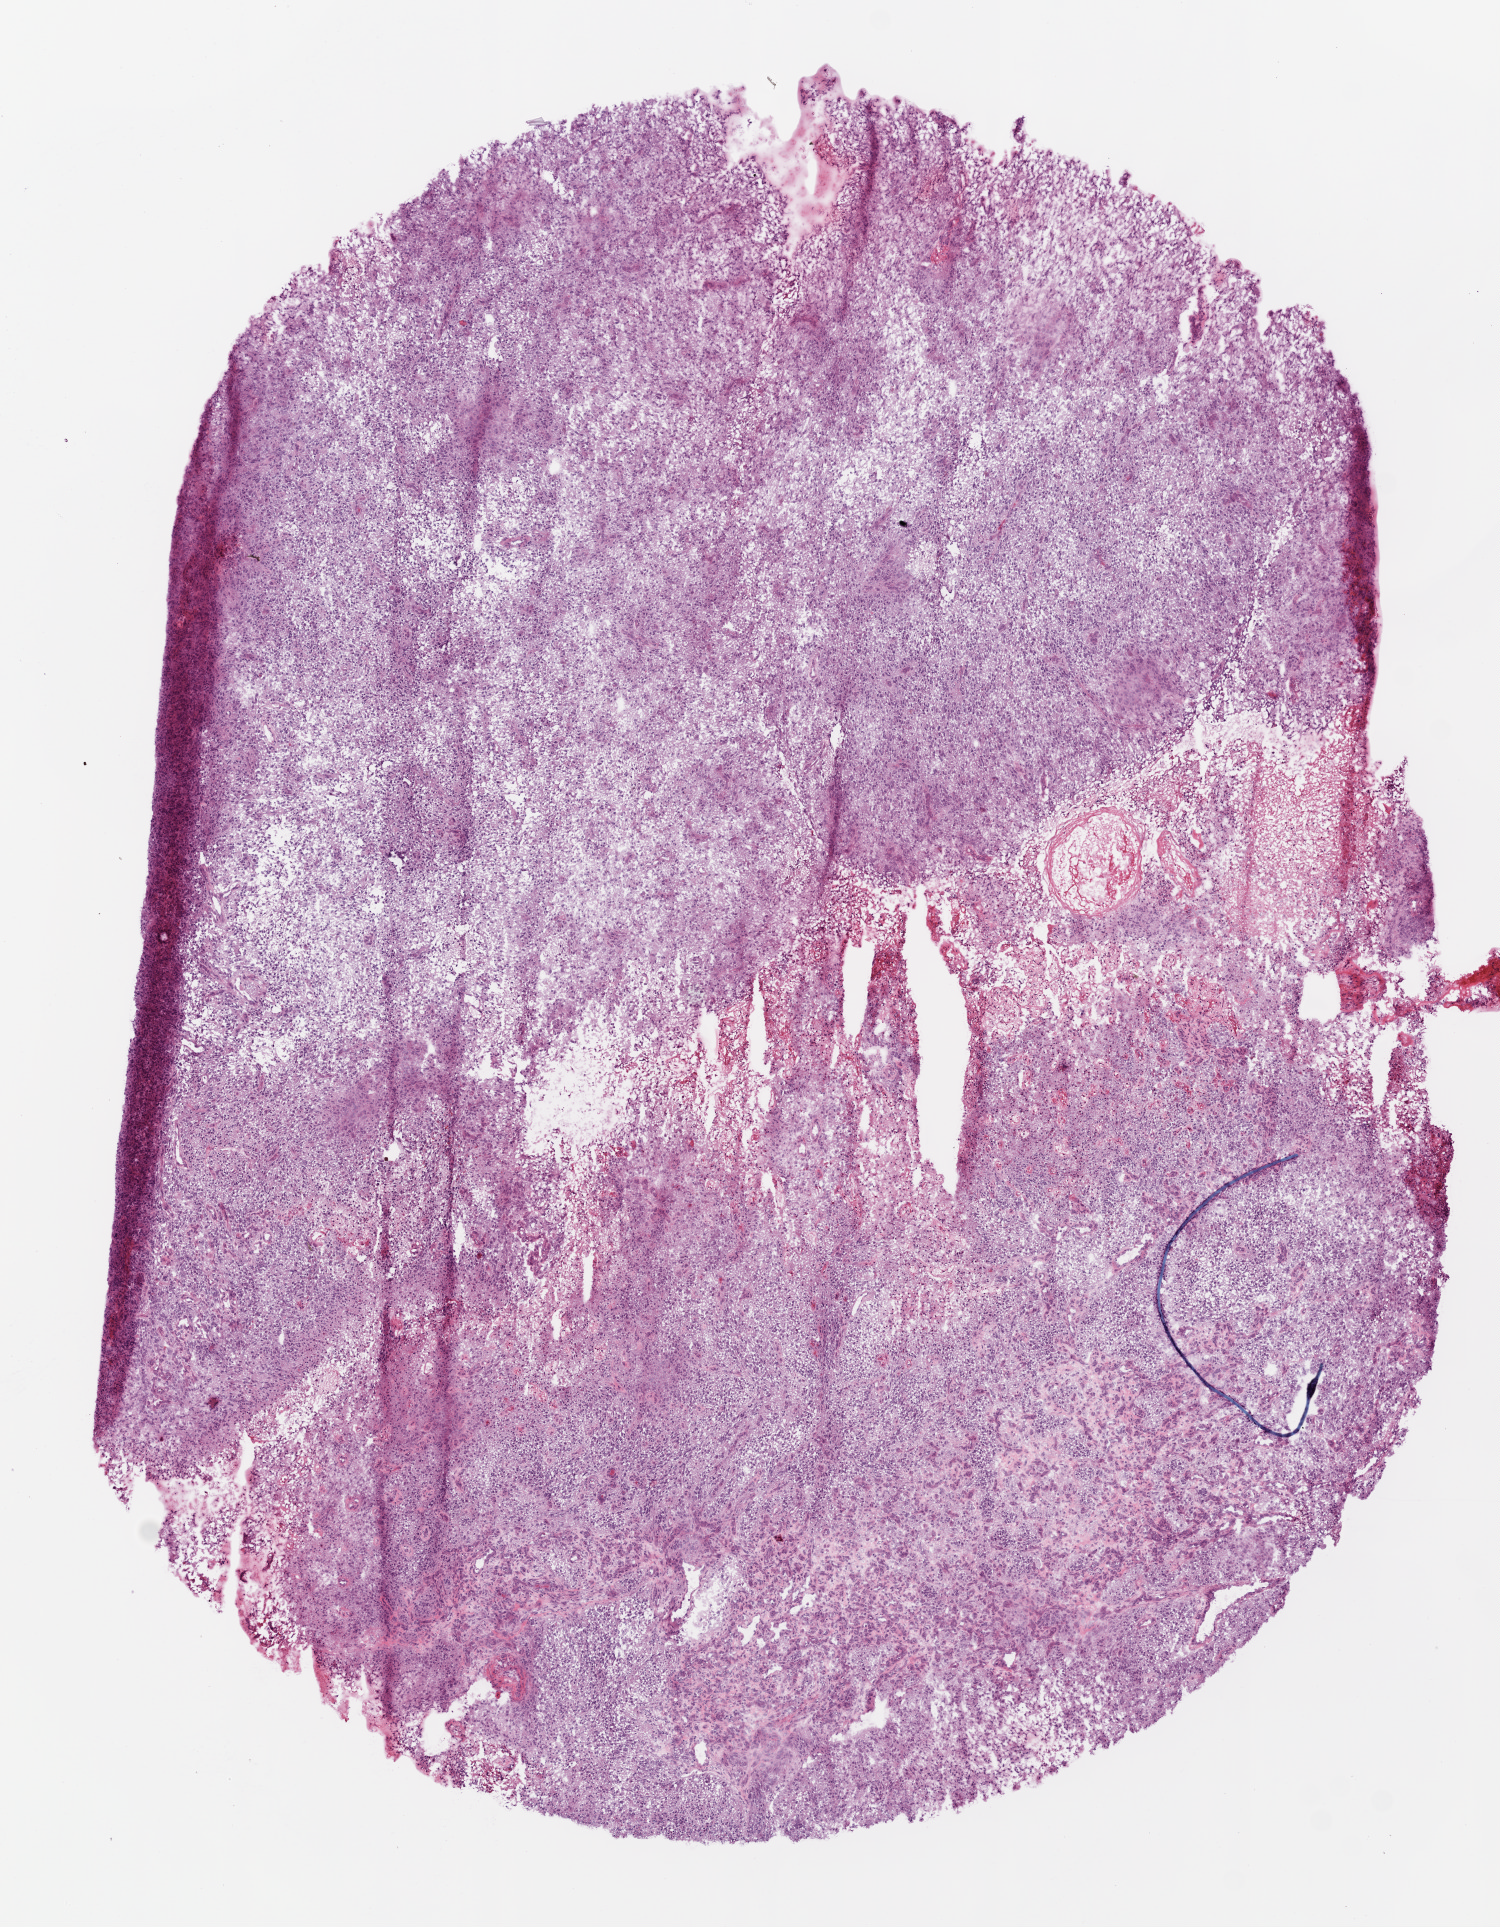
Whole-slide histology image, Hematoxylin and eosin (H&E) stained, low-resolution overview of the scanned area, about 6.0 x 7.7 mm. Frozen section. Brain, primary tumour sample. Male patient; age at initial diagnosis 81 years. Pathologist review of this section (percent, as recorded): tumour cells 99%, tumour nuclei 85%, normal cells 0%, stromal cells 0%, necrosis 1%.
Pathologic diagnosis: Glioblastoma.